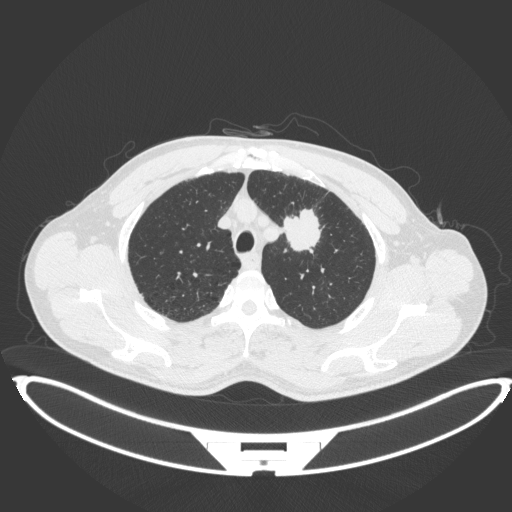
Chest CT, one axial slice. Position 352 of 407 along the scan axis. Lung window (W 1500 / L -600 HU). 512 × 512 image matrix, field of view 457 × 457 mm. Male patient, age 60 years. From the clinical record (not read from this slice): clinical TNM (as recorded): T2a N0 M0.
Outlined on this slice (bounding box drawn by a radiologist):
- lung tumour (recorded histology: squamous cell carcinoma): bounding box [x1, y1, x2, y2] px = [282, 205, 324, 256]